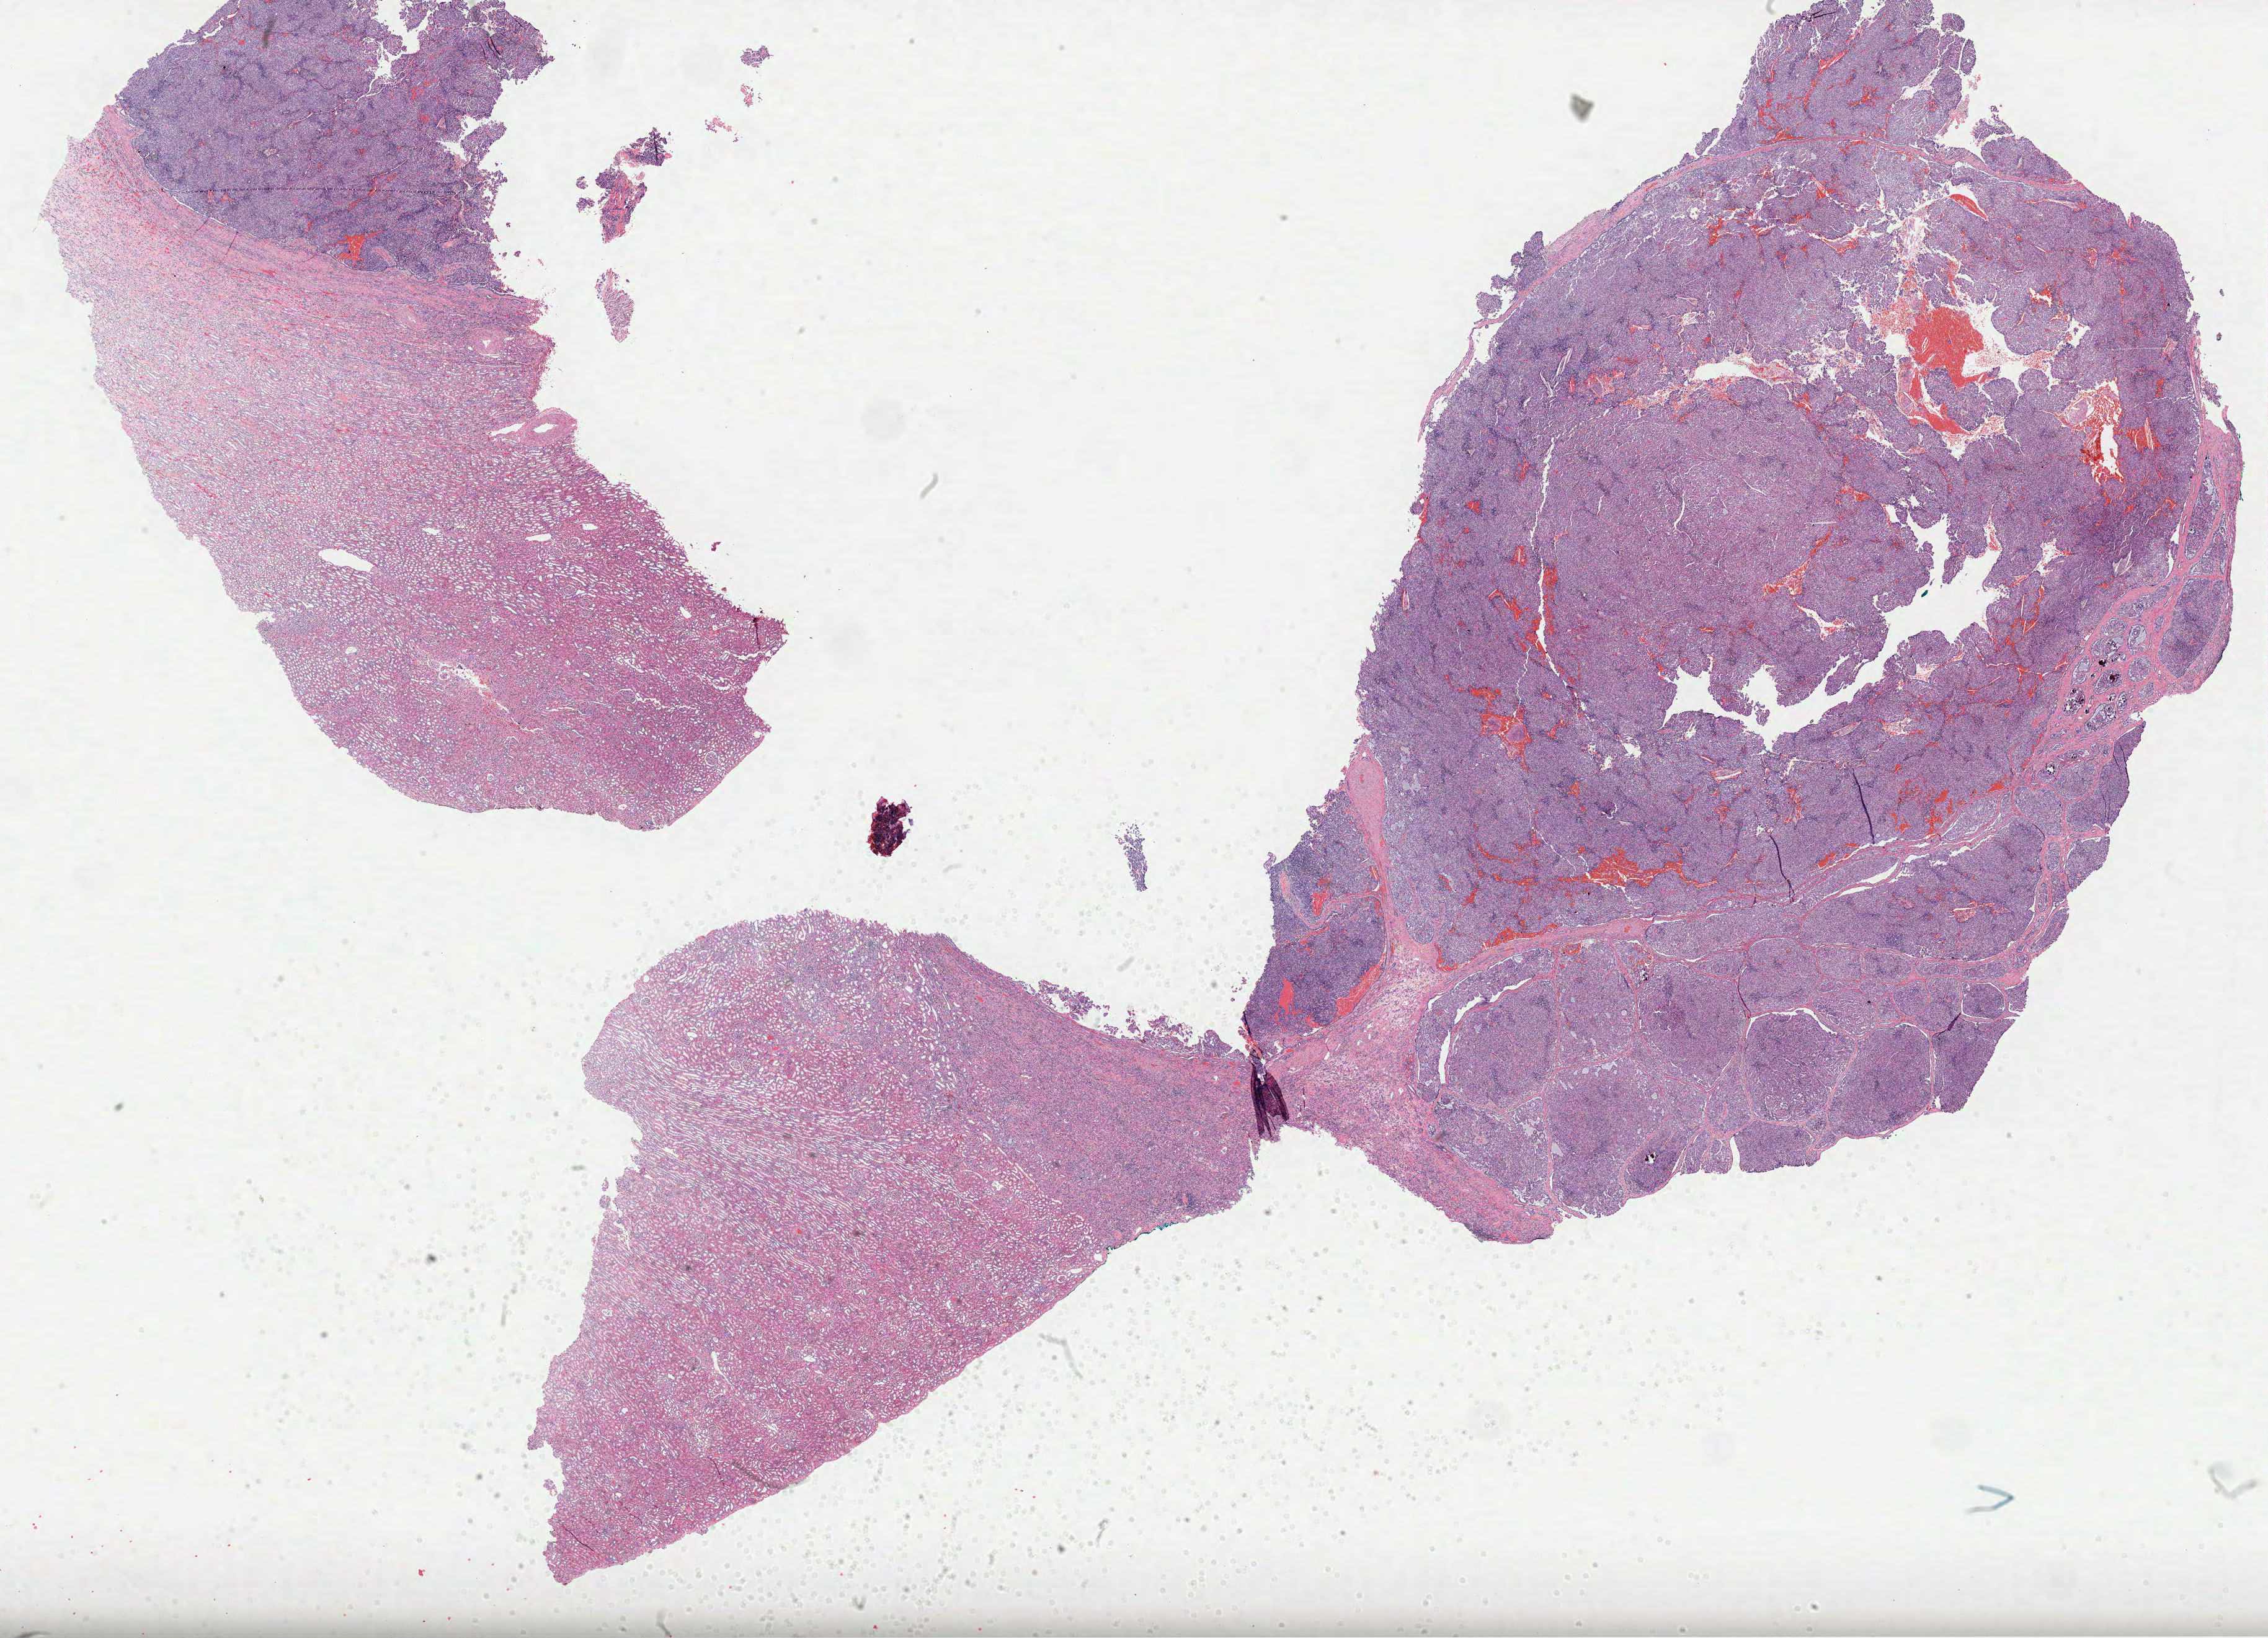
Whole-slide histology image, H&E, whole scanned area (about 29.5 x 21.3 mm) shown as a low-resolution overview, FFPE section, sample: primary tumour, kidney. Male, age 58 years at initial diagnosis.
Histologic diagnosis: Papillary adenocarcinoma, NOS. Laterality: left. AJCC pathologic stage: I (7th edition).